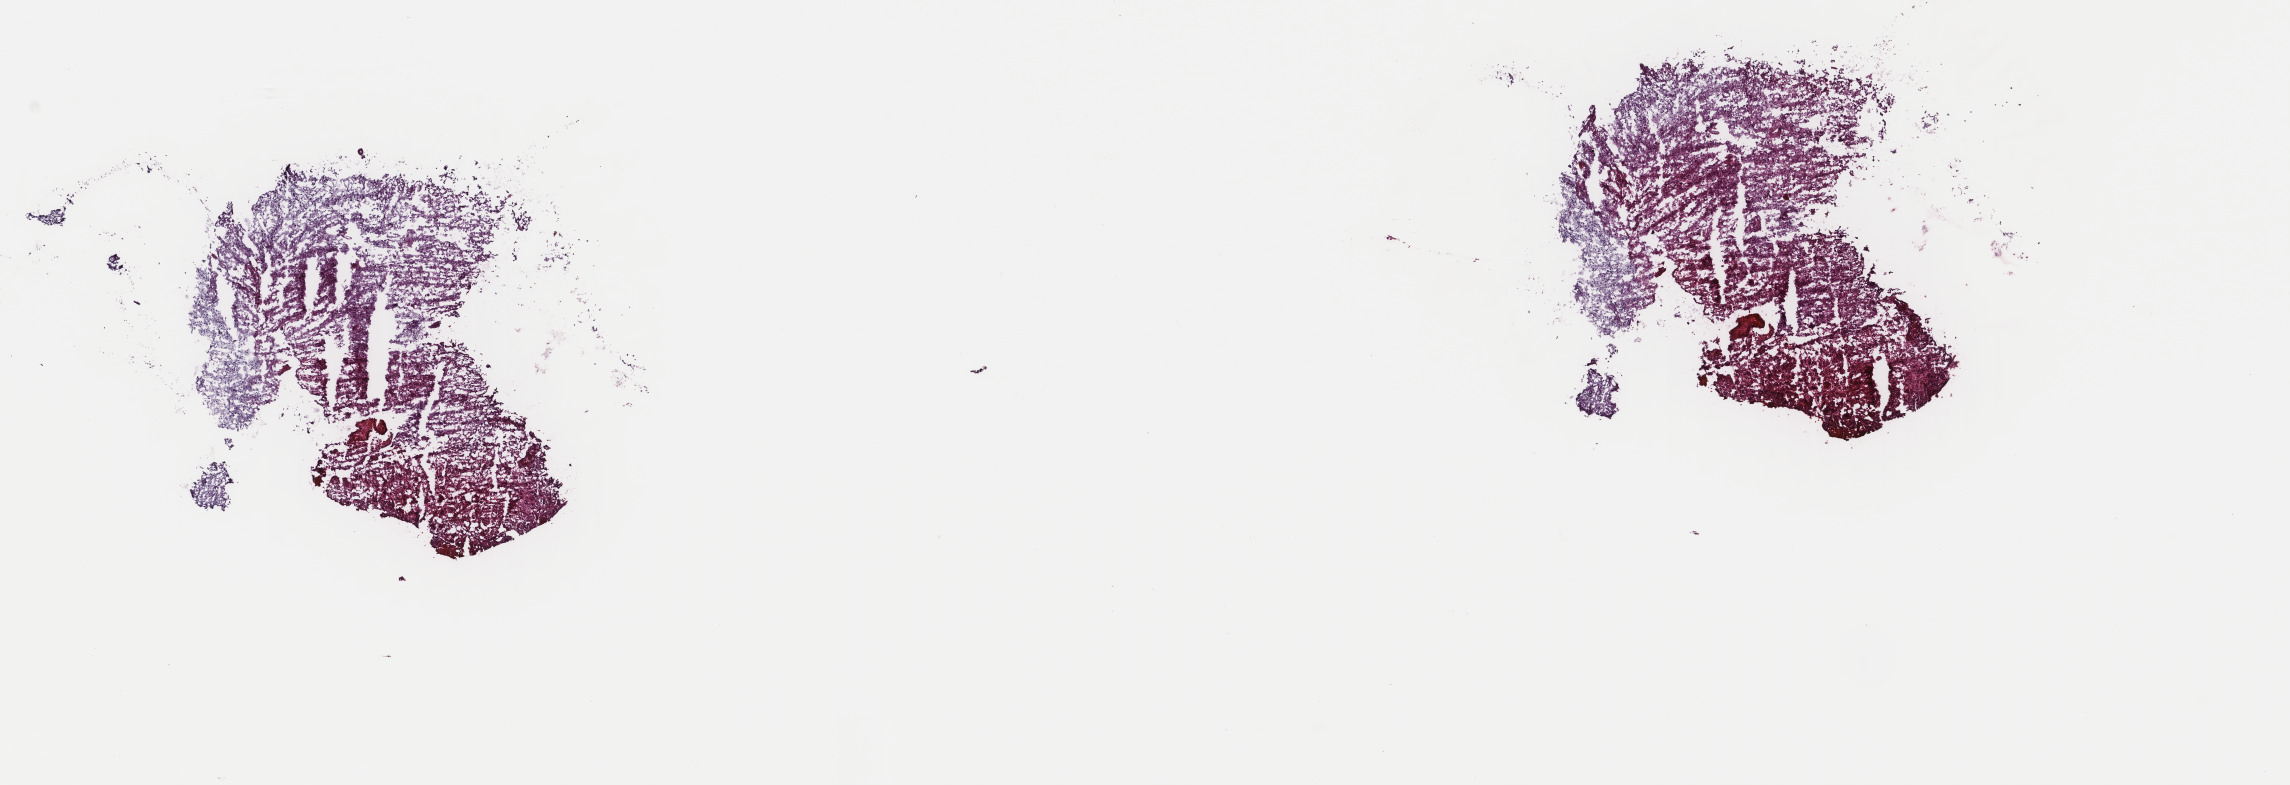
Whole-slide histology image, H&E-stained — a low-resolution overview of the entire scanned area, about 18.2 x 6.2 mm (acquisition: 40x scan), frozen section from the top of the tissue portion, sample: primary tumour, brain. Patient: male, age at initial diagnosis 55 years. Composition of this section per pathologist review: tumour cells 60%, tumour nuclei 85%, normal cells 20%, stromal cells 20%, necrosis 0%. Infiltration values recorded for this section: lymphocyte infiltration 0%, monocyte infiltration 0%, neutrophil infiltration 0%.
Histologic diagnosis: Glioblastoma (temporal lobe).